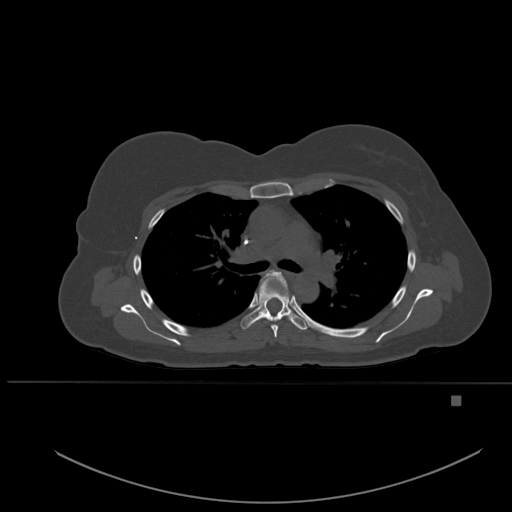
CT including the spine, one axial slice; slice 370 of 651 in the series (ordered by position); bone window (W 1800 / L 400 HU); 1.5 mm slice thickness; 512 × 512 image matrix. Patient: female, 49 years. Case-level facts recorded for this patient, not image findings: primary cancer: breast.
Outlined on this slice (semi-automatically segmented with operator editing):
- T4 vertebra: bounding box (x1, y1, x2, y2) in pixels: (264, 270, 287, 338)
- T5 vertebra: (240, 276, 307, 330)